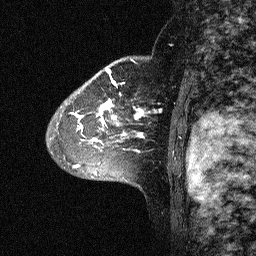
Breast MRI (dynamic contrast-enhanced), one sagittal slice; position 45 of 64 along the scan axis; dynamic contrast-enhanced study with each time point stored as its own series, time point 2 of 3 at this slice position (early post-contrast, ordered by acquisition time); 1.5 T; TE 4.5 ms, TR 11 ms; 2.06 mm slice thickness; 256 × 256 image matrix, field of view 200 × 200 mm. Female patient, age 46 years. Case-level facts recorded for this patient, not image findings: setting: breast cancer imaged before/during neoadjuvant chemotherapy; receptor status: HER2-positive.
Structures marked on this image (semi-automatically segmented with operator editing):
- analysis volume of interest (the breast-tissue region the enhancement analysis was run in; not a lesion): bounding box [x1, y1, x2, y2] px = [43, 72, 164, 177]
- tumour enhancement mask (voxels above the 90 % enhancement threshold inside the analysis volume of interest): [71, 72, 162, 167]